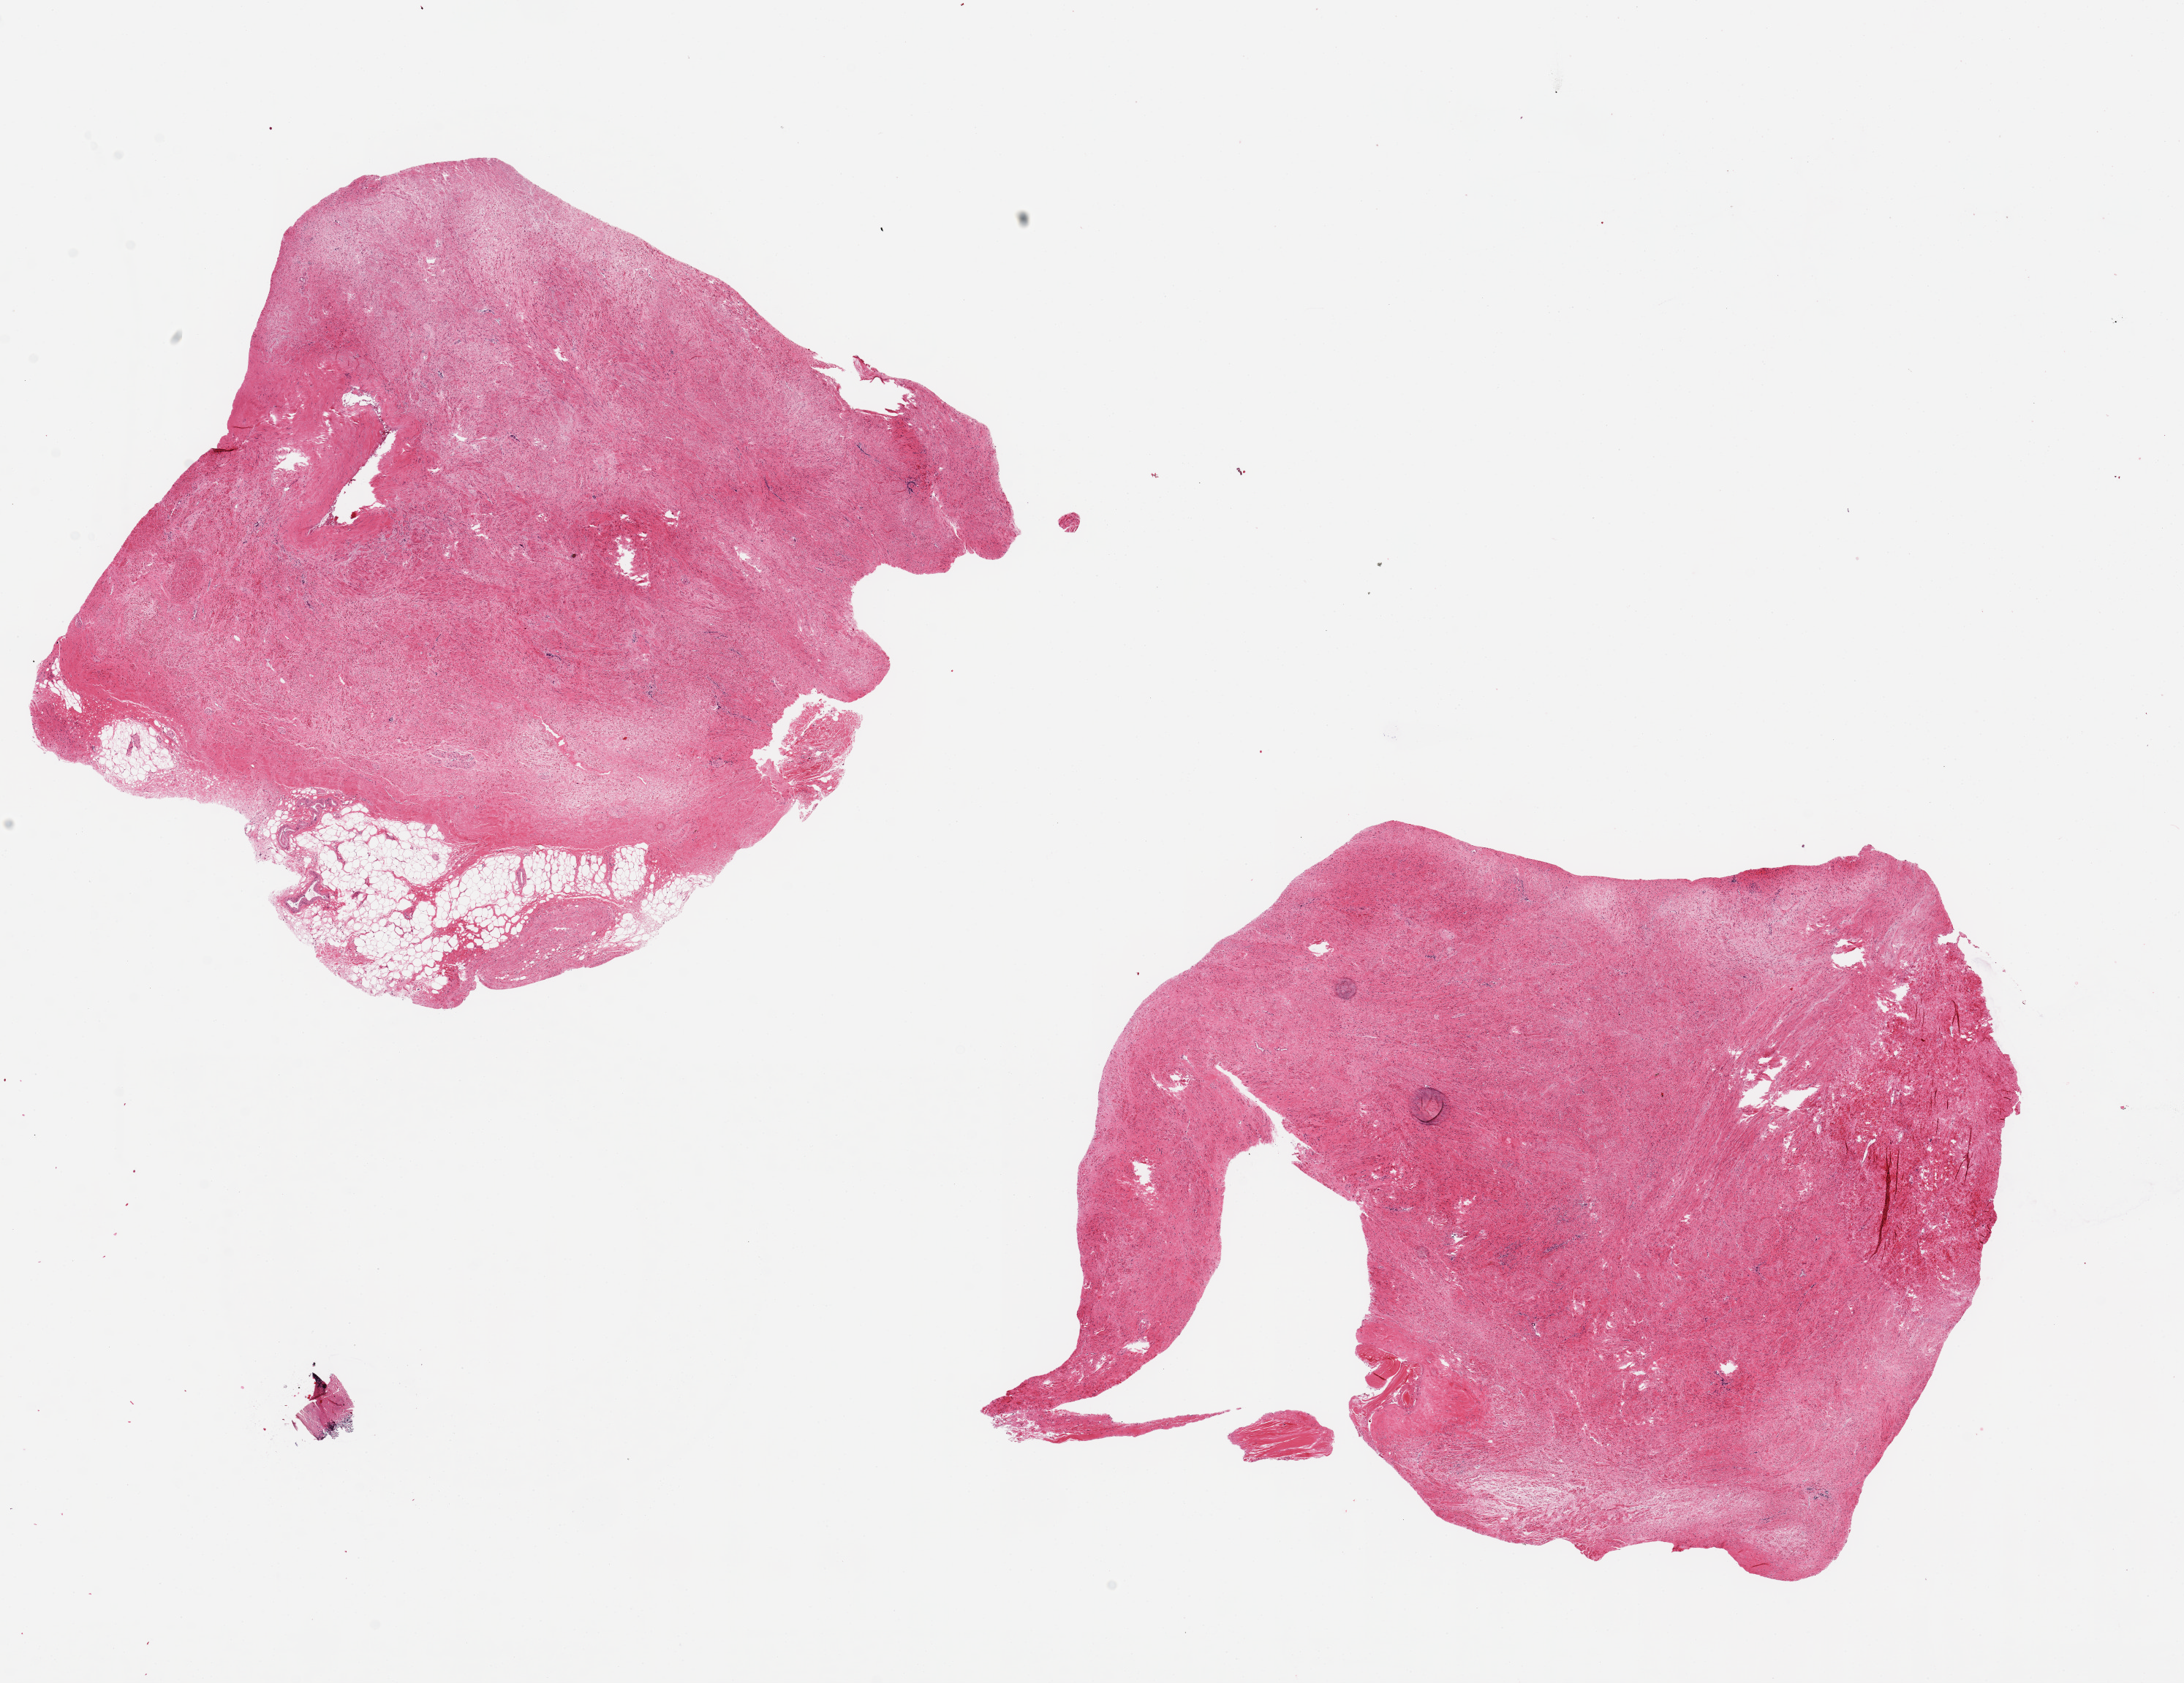
Digitized H&E-stained section, whole scanned area (about 23.6 x 18.2 mm) shown as a low-resolution overview, PAXgene-fixed paraffin-embedded (PFPE) section, section of prostate (target tissue), tissue donor sample.
Reviewer comment on this tissue sample: 2 ~8x8mm pieces, all stroma, no glandular component present. ?stromal nodule vs exuberant.